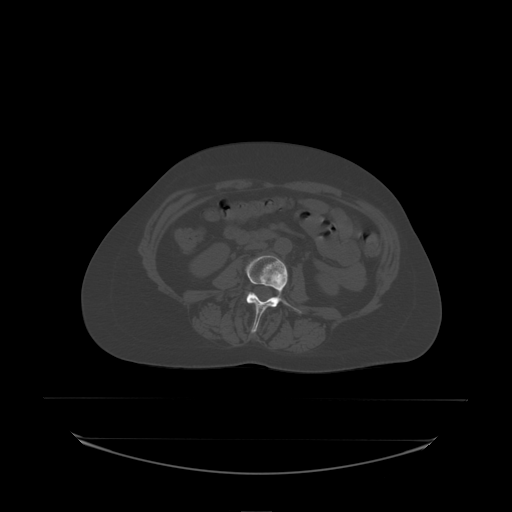
CT including the spine, one axial slice. Position 60 of 242 along the scan axis. Bone window (W 1800 / L 400 HU). 2.5 mm slice thickness. 512 × 512 image matrix, field of view 500 × 500 mm. Patient: female, 53 years. From the clinical record (not read from this slice): primary cancer: lung.
Outlined on this slice (semi-automatic segmentation, software-assisted and operator-edited):
- L3 vertebra: bounding box (x1, y1, x2, y2) in pixels: (246, 256, 302, 334)